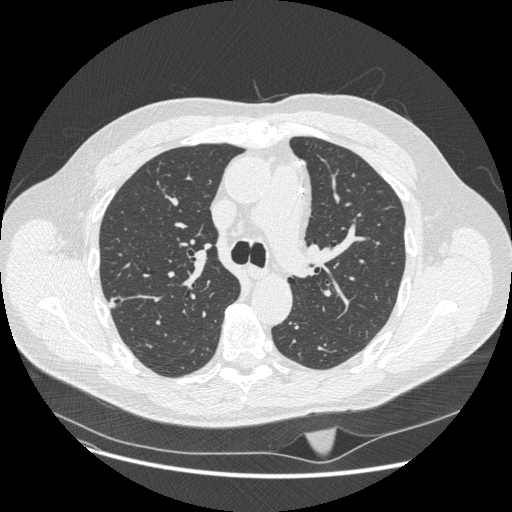
Axial slice from a low-dose chest CT screening exam; second annual screen; lung window (W 1500 / L -600 HU); 1.25 mm slice thickness; standard (soft-tissue) reconstruction kernel (STANDARD); 120 kVp; slice 76 of 247 in the series. Male, age 62 years at enrolment. Current smoker at enrolment.
Expert reader's lesion annotation, box from (x=98, y=290) to (x=130, y=318) px. Reader record for this screening exam (exam-level; its link to the box is not recorded): non-calcified nodule or mass ≥4 mm, right upper lobe, 11 × 7 mm, smooth margins, pre-existing on the prior screen: yes. Official screen result: positive, change unspecified: nodule(s) >= 4 mm or enlarging nodule(s), mass(es), or other non-specific abnormalities suspicious for lung cancer. Lung cancer was diagnosed 482 days after this screen (after the third annual screen): adenocarcinoma, NOS, right upper lobe, moderately differentiated (G2), stage IA (AJCC 6th edition), 12 mm at pathology.